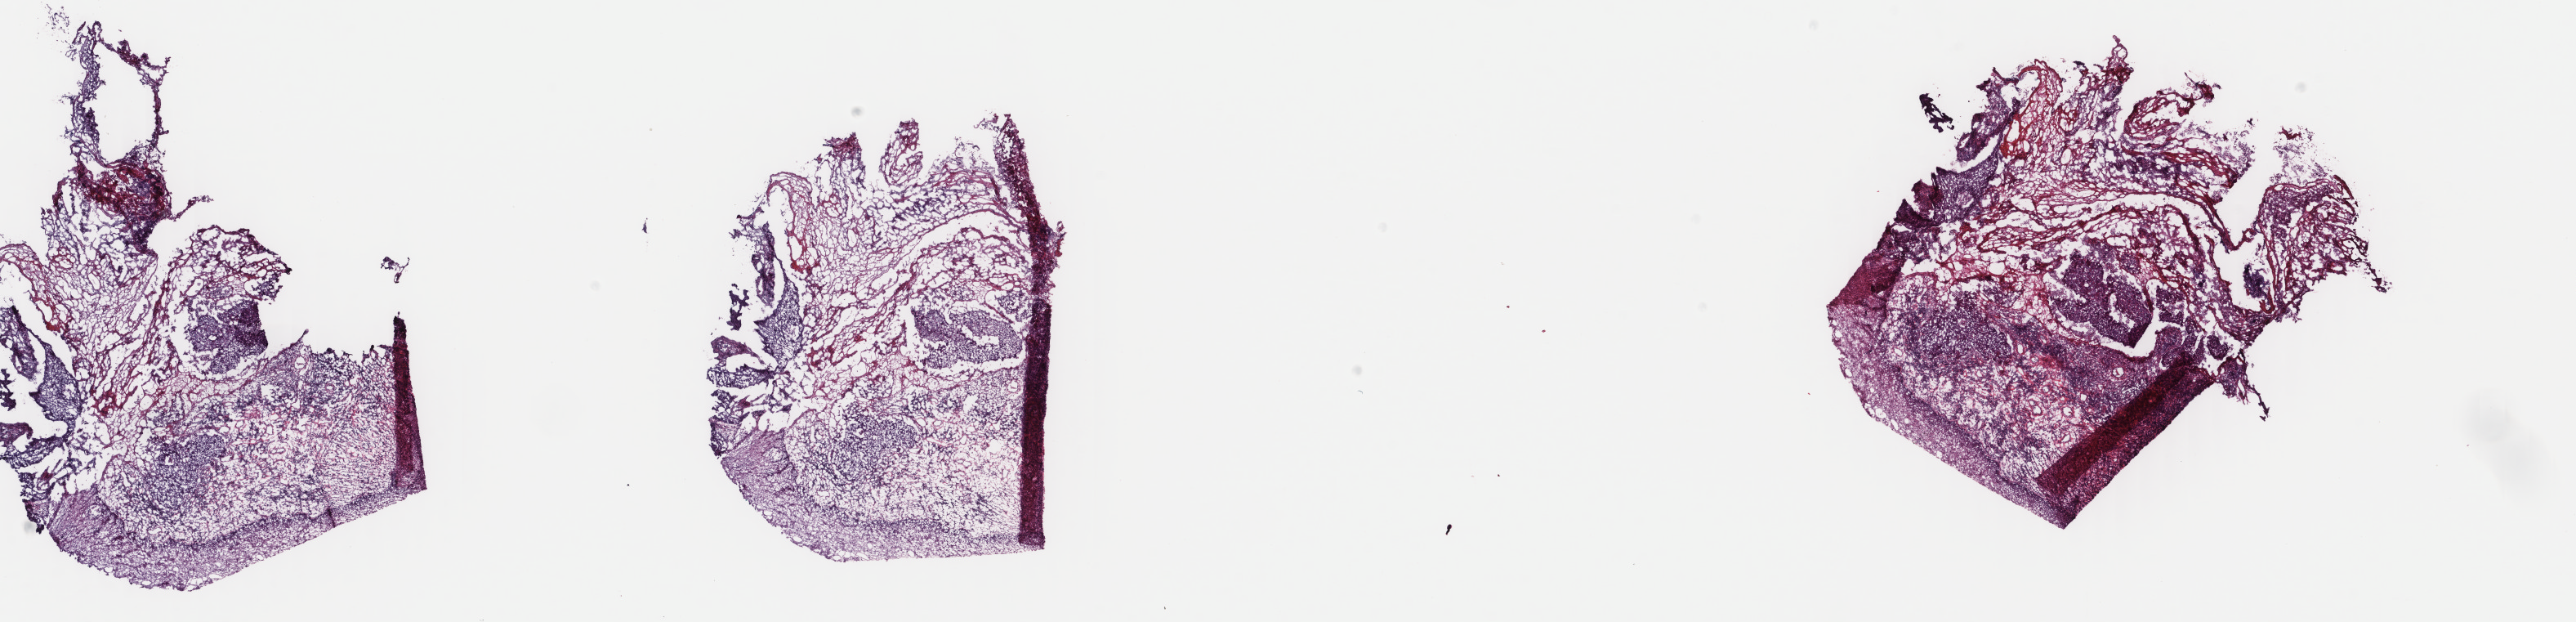
H&E whole-slide image, low-resolution overview of the scanned area, about 25.0 x 6.0 mm (from a 40x scan). Frozen section. Sample: primary tumour, cervix. Female, age 53 years at initial diagnosis. Histologic grade: G3 (poorly differentiated). Slide review estimates, as recorded: tumour cells 25%, tumour nuclei 6%, normal cells 60%, stromal cells 12%, necrosis 3%. Inflammatory infiltration, as recorded: lymphocyte infiltration 35%, monocyte infiltration 1%, neutrophil infiltration 40%.
Diagnosis: Squamous cell carcinoma, NOS (cervix uteri). Lymph nodes positive (case pathology): 0 of 24 examined. FIGO stage: IB.